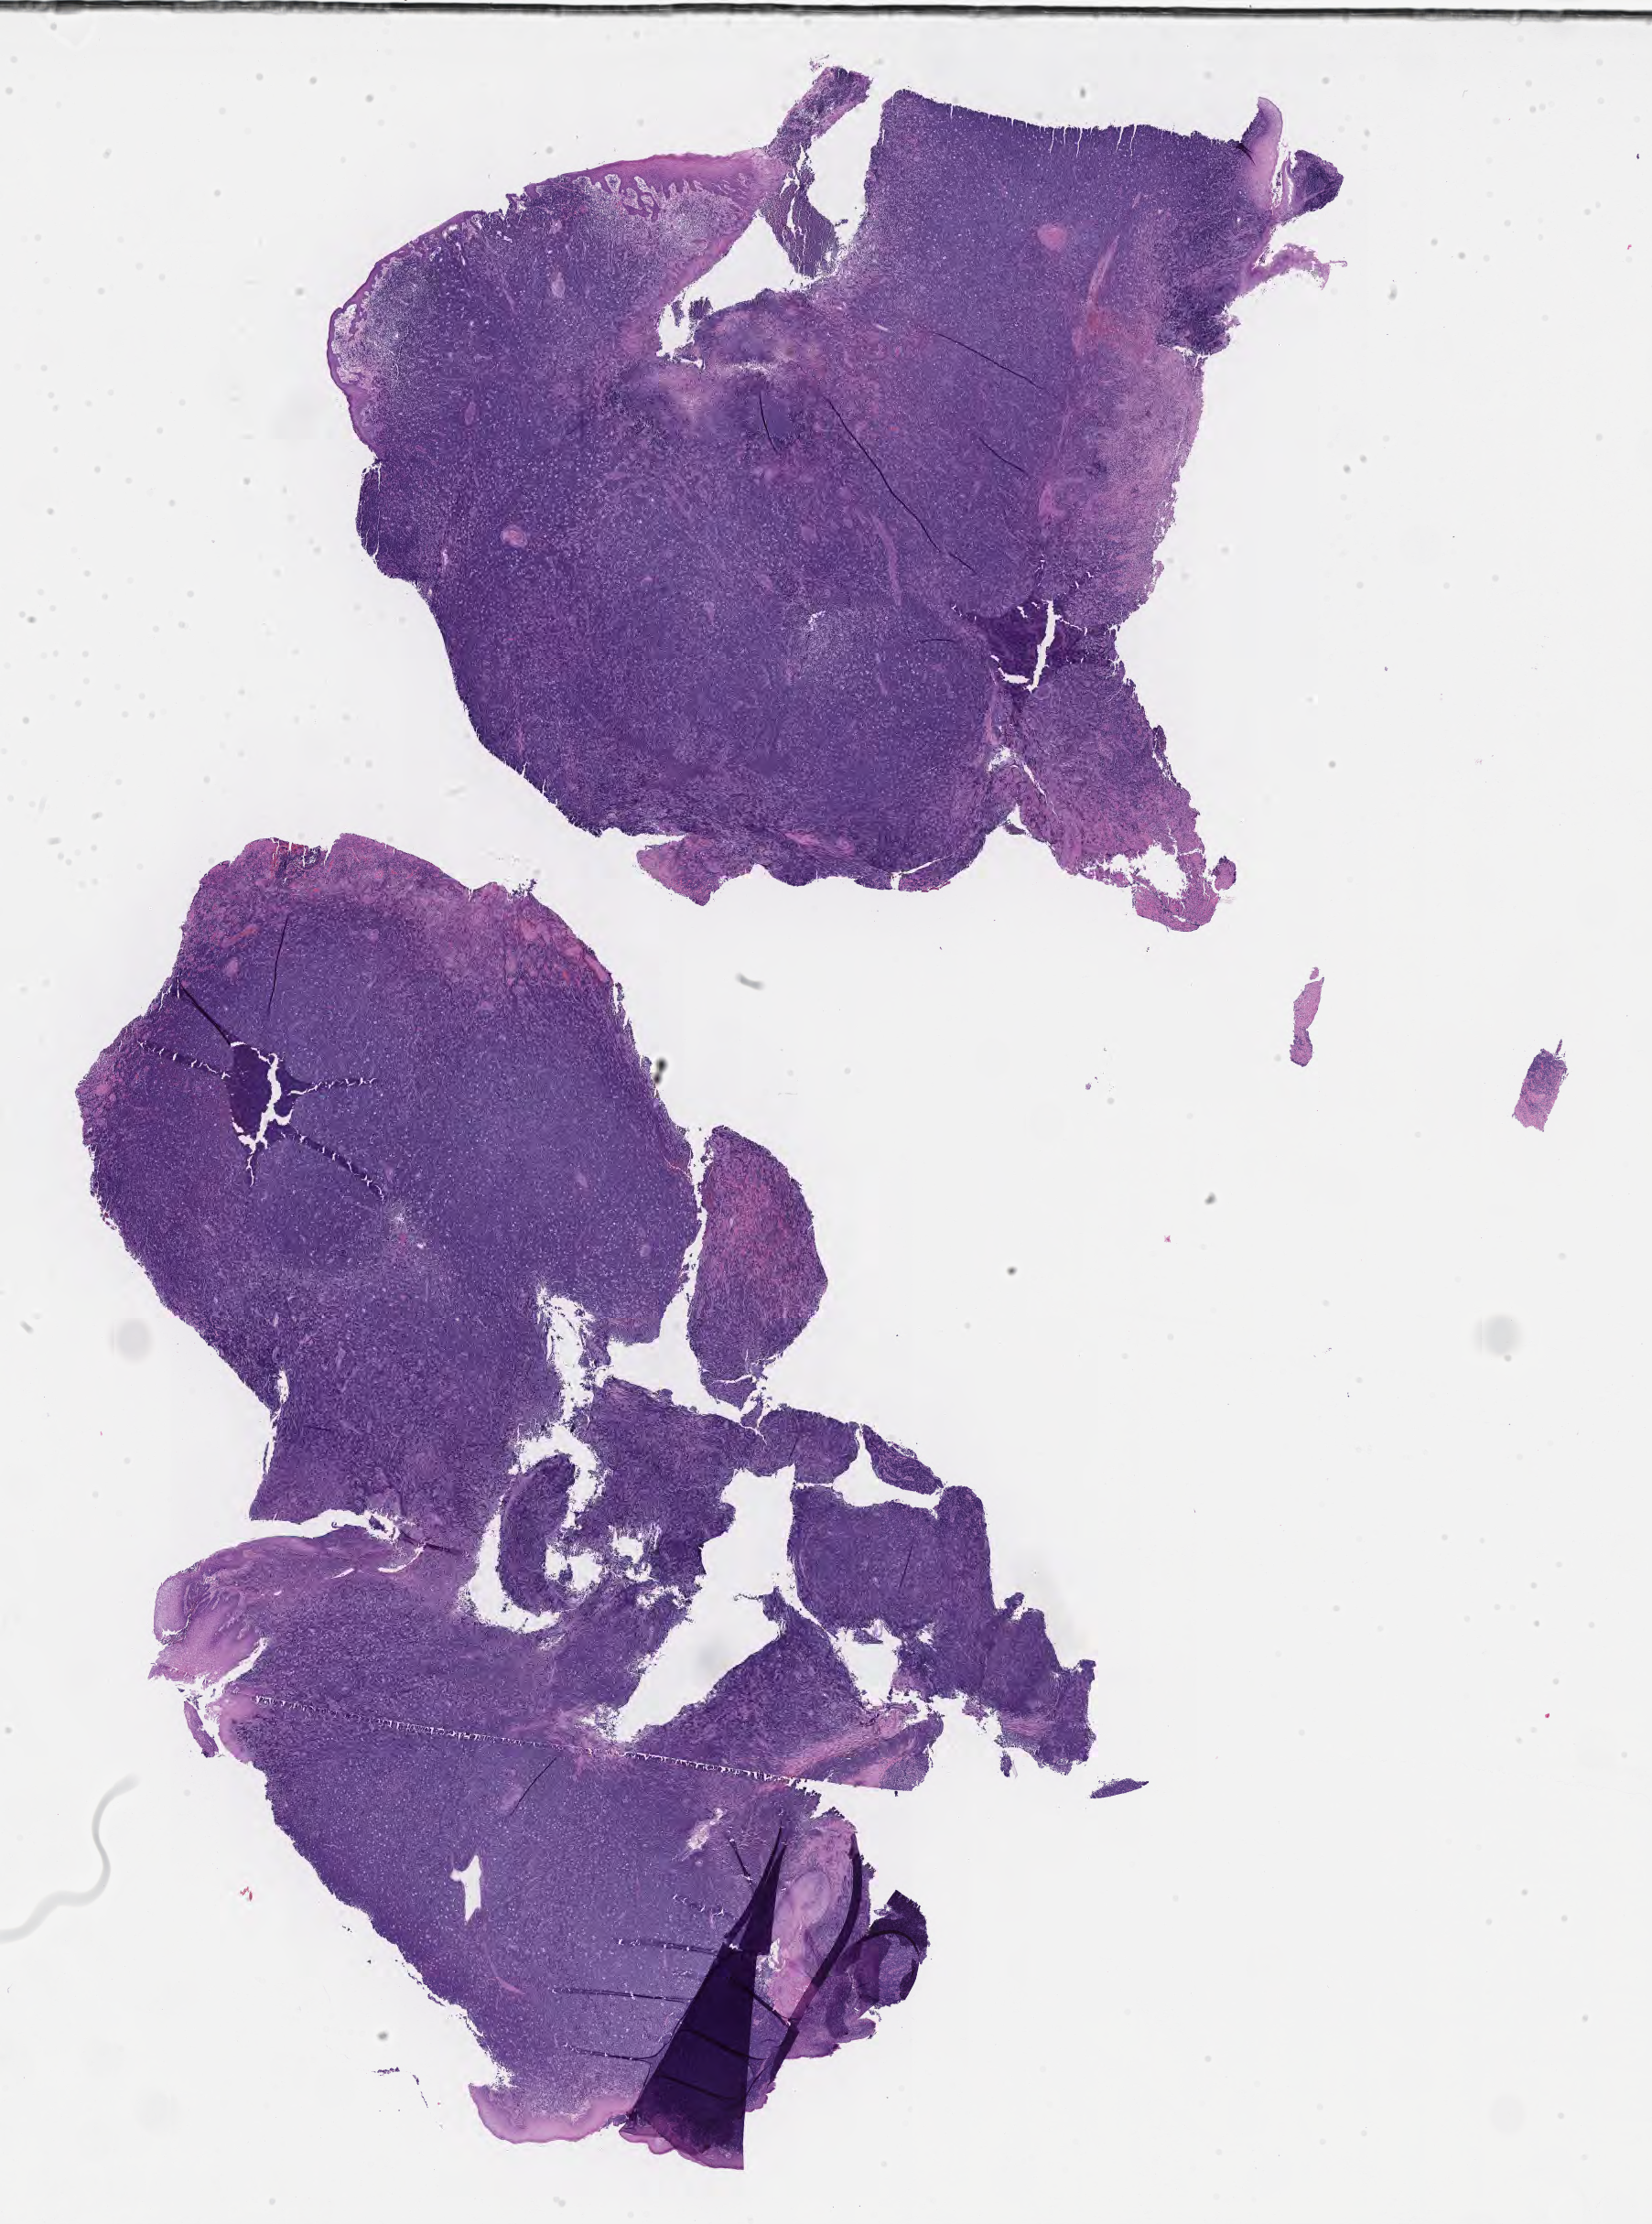
Whole-slide image, hematoxylin and eosin (H&E) stain, low-resolution overview of the scanned area, about 14.6 x 19.6 mm; tumor tissue. Patient: male, aged 22.
Histologic diagnosis: Diffuse large B-cell lymphoma, NOS.